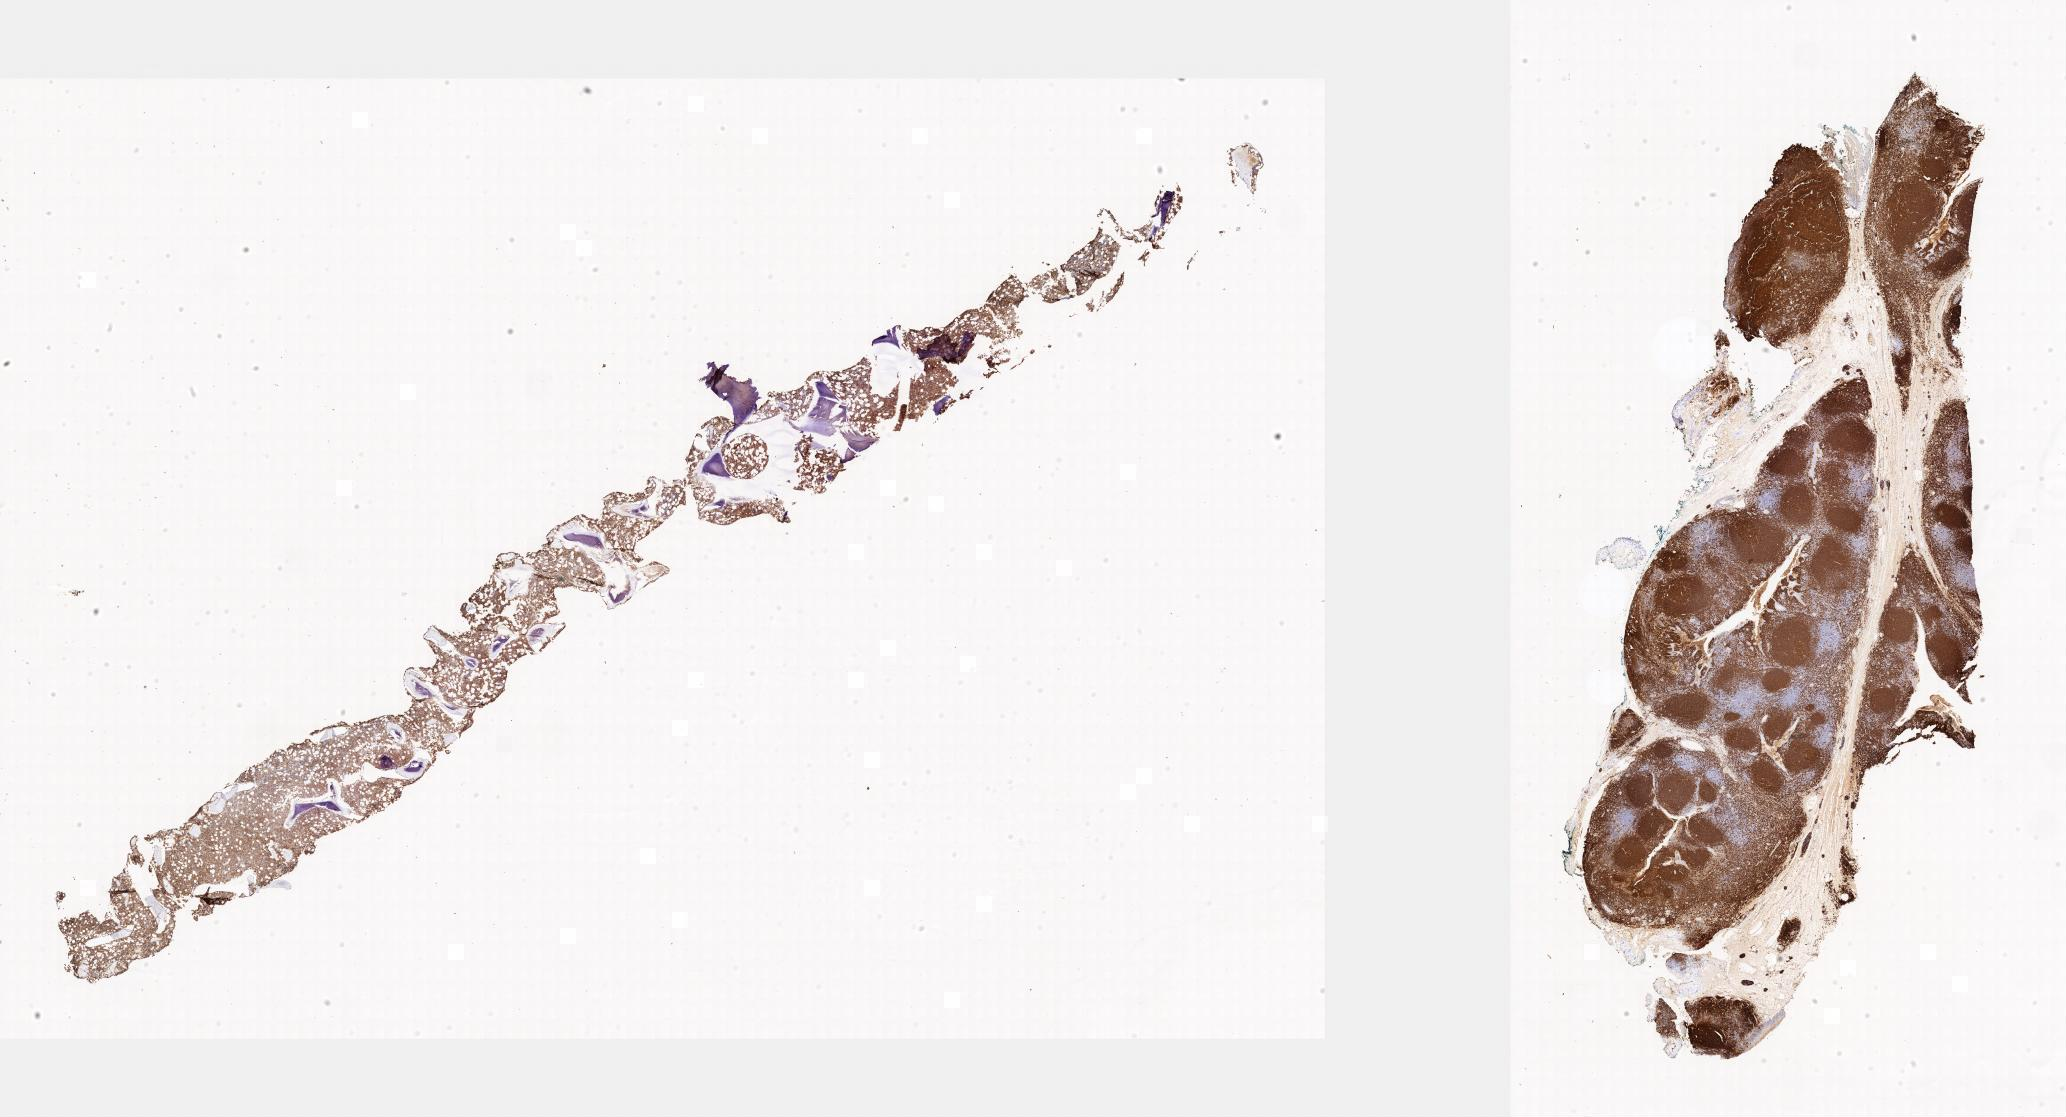
Immunohistochemistry (IHC) whole-slide image stained for CD20, shown as a low-resolution overview of the whole scanned area; specimen: tumor tissue; anatomic site: bone marrow. Patient male; aged 20.
Histologic diagnosis: Diffuse large B-cell lymphoma, NOS.